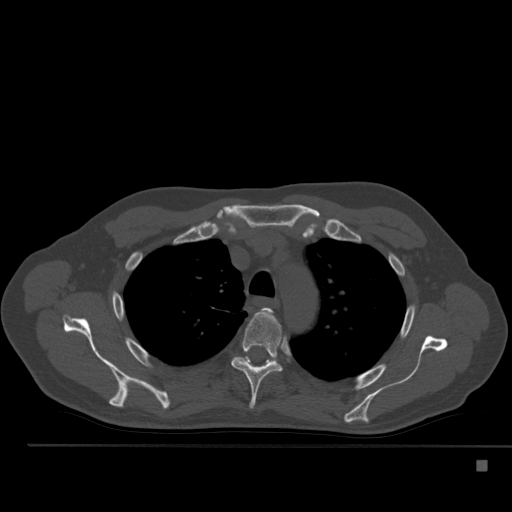
CT including the spine, one axial slice; slice 381 of 517 in the series (ordered by position); 120 kVp; bone window (W 1800 / L 400 HU); 1.5 mm slice thickness; 512 × 512 image matrix, field of view 408 × 408 mm. Male patient, age 70 years. Case-level facts recorded for this patient, not image findings: primary cancer: renal.
Structures marked on this image (semi-automatic segmentation, software-assisted and operator-edited):
- T3 vertebra: box from (x=263, y=308) to (x=272, y=312) px
- T4 vertebra: (x=231, y=309)–(x=282, y=409)
- T5 vertebra: (x=242, y=357)–(x=272, y=362)